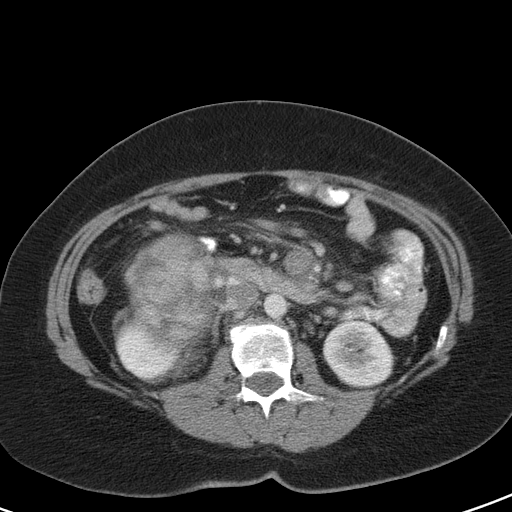
Contrast-enhanced abdominal CT, one axial slice; slice 59 of 126 in the series (ordered by position); 120 kVp; intravenous contrast given; soft-tissue window (W 400 / L 40 HU); 512 × 512 image matrix, field of view 356 × 356 mm. Female patient, age 51 years. Case-level facts recorded for this patient, not image findings: diagnosis: adrenocortical carcinoma; tumour side: right adrenal; tumour size at pathology: 17 cm; Ki-67 index: 12 %; stage (as recorded): 2.
Structures marked on this image (semi-automatic segmentation, software-assisted and operator-edited):
- mass: bounding box (x1, y1, x2, y2) in pixels: (125, 236, 215, 344)